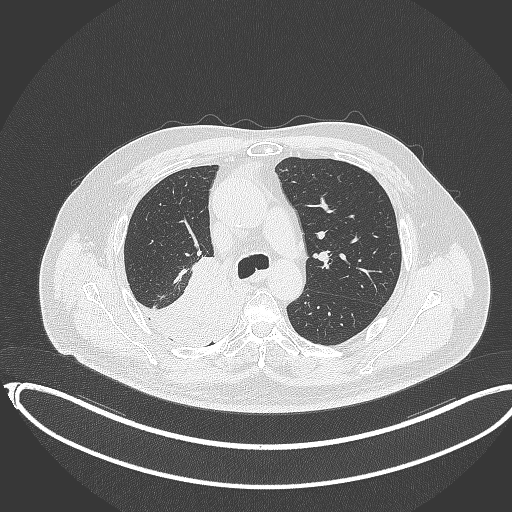
Chest CT, one axial slice; slice 241 of 403 in the series (ordered by position); reconstruction kernel B70f; 120 kVp; lung window (W 1500 / L -600 HU); 1 mm slice thickness; 512 × 512 image matrix, field of view 436 × 436 mm. Patient: male, 68 years. Case-level facts recorded for this patient, not image findings: clinical TNM (as recorded): T2a N0 M0.
Structures marked on this image (bounding box drawn by a radiologist):
- lung tumour (recorded histology: adenocarcinoma): bounding box <126,241,243,342> (left, top, right, bottom; pixels)